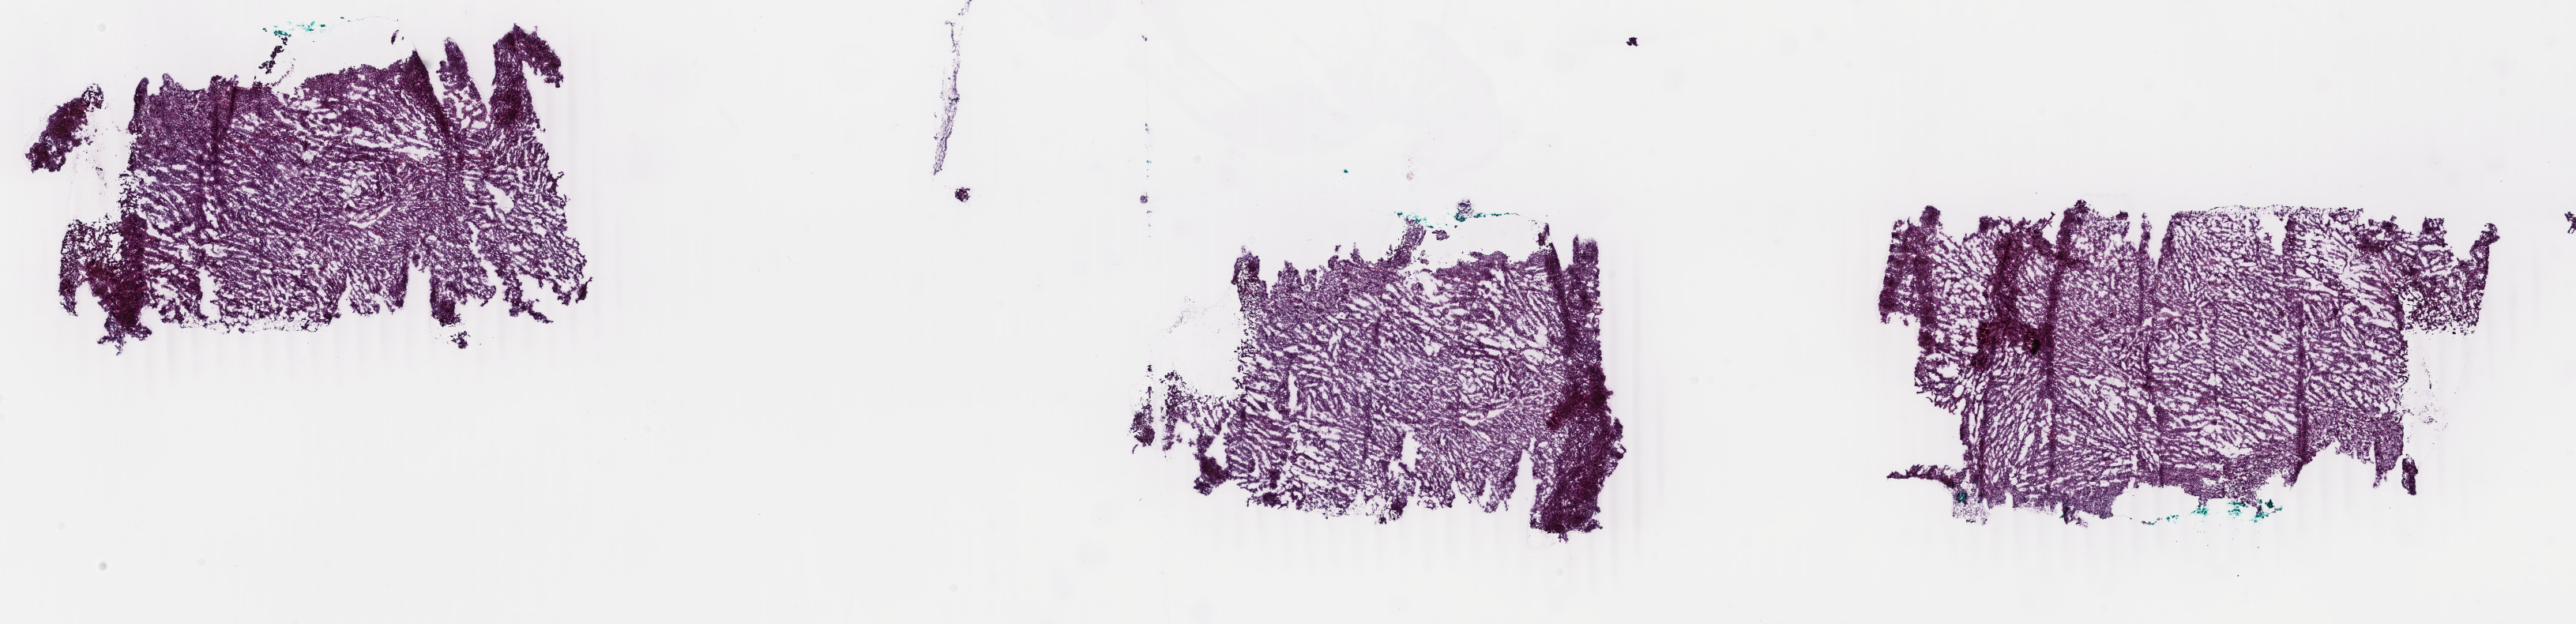
Whole-slide histology image, Hematoxylin and eosin (H&E) stained — whole scanned area (about 25.9 x 6.3 mm, slide scanned at 40x) shown as a low-resolution overview. Frozen section. Sample: primary tumour, uterus. Female patient; age at initial diagnosis 69 years.
Pathologic diagnosis: Endometrioid adenocarcinoma, NOS (endometrium).